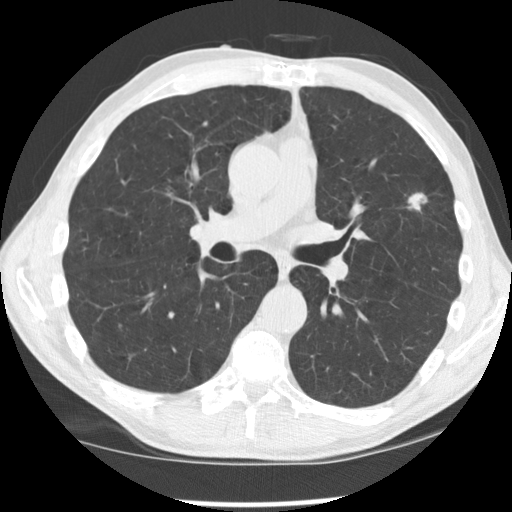
Axial slice from a low-dose chest CT screening exam. Second screening round (one year after baseline). Lung window (W 1500 / L -600 HU). Standard (soft-tissue) reconstruction kernel (STANDARD). Slice 74 of 170 in the series. Male participant, aged 64 years at enrolment.
- Expert-annotated lung lesion, bounding box <387,178,442,224> (left, top, right, bottom; pixels).
- Reader record for this screening exam (exam-level; its link to the box is not recorded): non-calcified nodule or mass ≥4 mm, left upper lobe, 16 × 11 mm, spiculated (stellate) margins, soft tissue attenuation, pre-existing on the prior screen: yes; interval growth: yes.
- Official screen result: positive, other.
- Later outcome: lung cancer diagnosed 59 days after this screen — adenocarcinoma, NOS, left upper lobe, poorly differentiated (G3), stage IA (AJCC 6th edition), 10 mm at pathology.